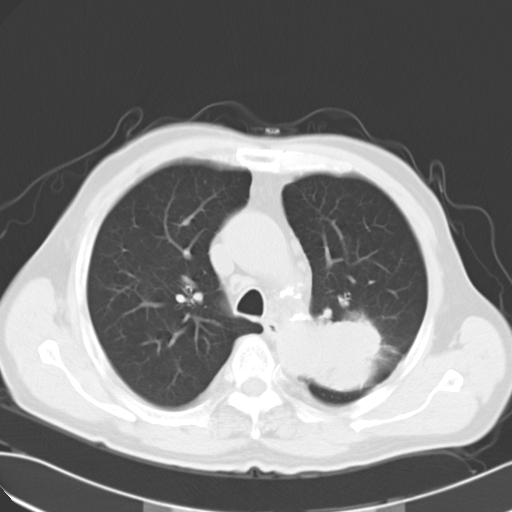
Chest CT, one axial slice. Slice 20 of 28 in the series (ordered by position). Reconstruction kernel B40f. Lung window (W 1500 / L -600 HU). 10 mm slice thickness. 512 × 512 image matrix, field of view 353 × 353 mm. Patient: male, 63 years. Case-level facts recorded for this patient, not image findings: clinical TNM (as recorded): T3 N3 M1a; histopathological grade: G3.
Outlined on this slice (bounding box drawn by a radiologist):
- lung tumour (recorded histology: large cell carcinoma): bounding box <293,300,387,399> (left, top, right, bottom; pixels)